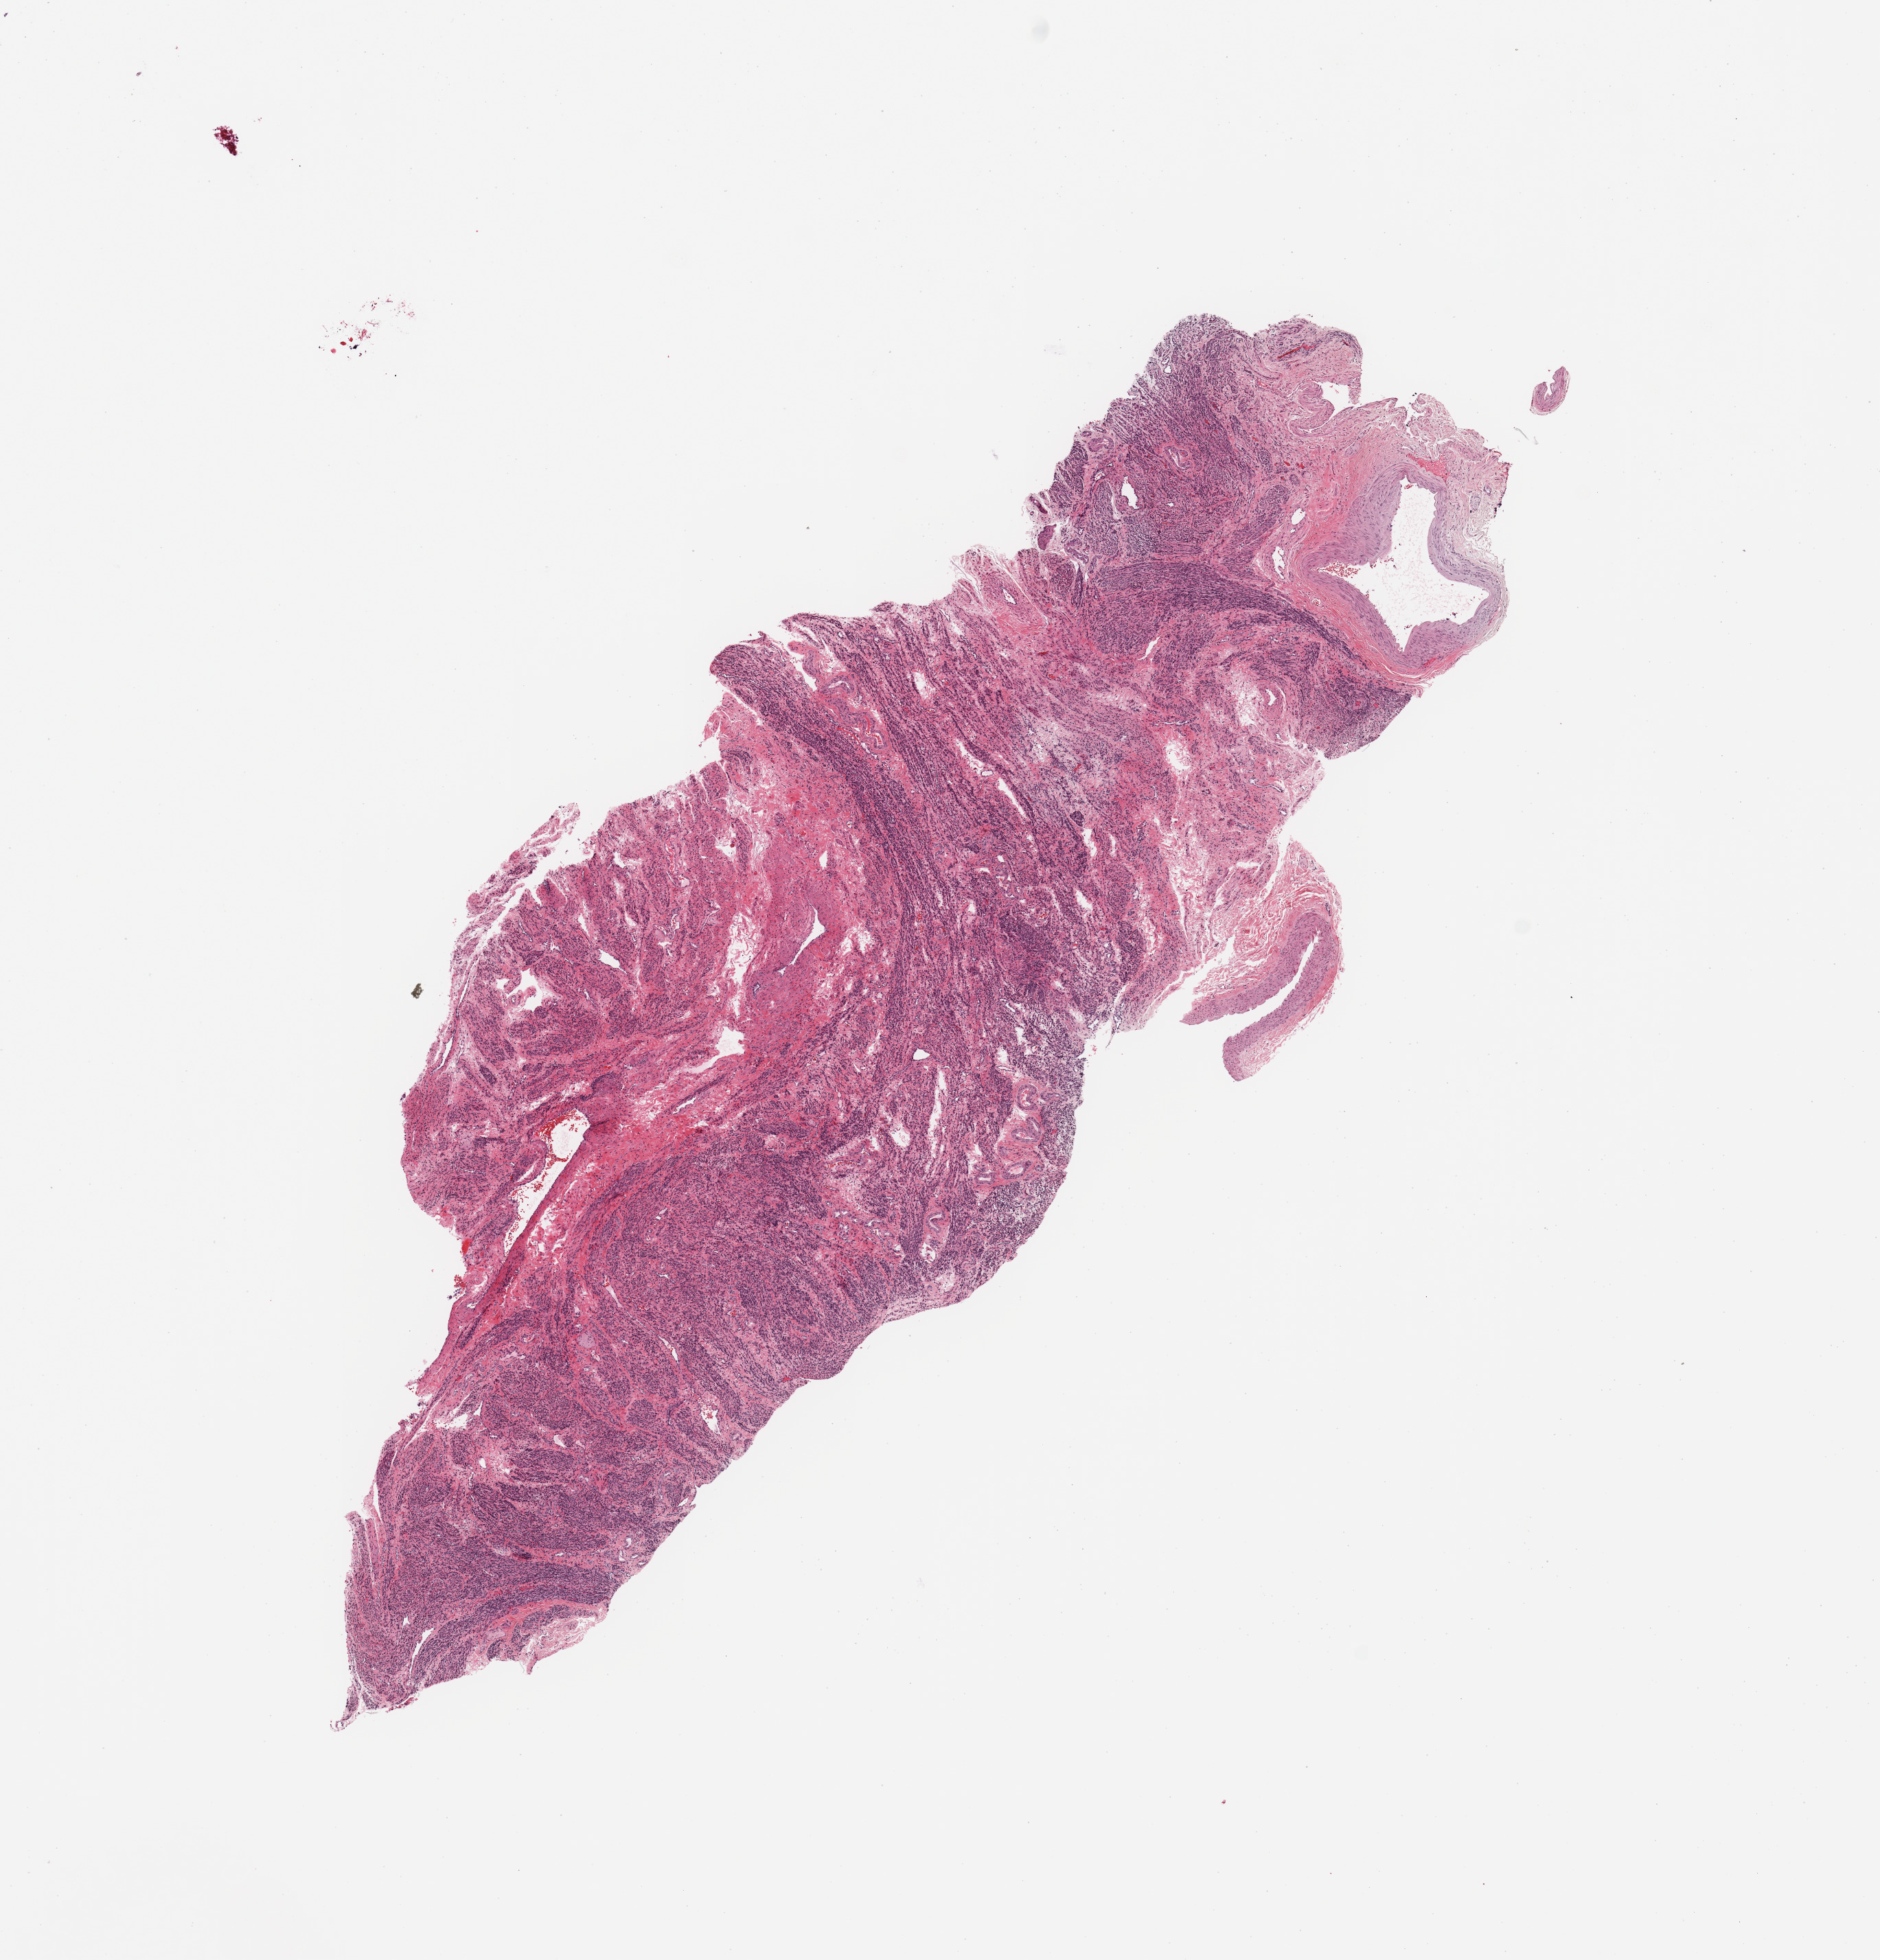
H&E whole-slide image — low-resolution overview of the scanned area, about 10.8 x 11.3 mm, uterus, normal (non-tumour) tissue. Patient: female, age 65 years.
This section: normal (non-tumour) tissue from the same patient. Patient diagnosis: Endometrioid adenocarcinoma, NOS.